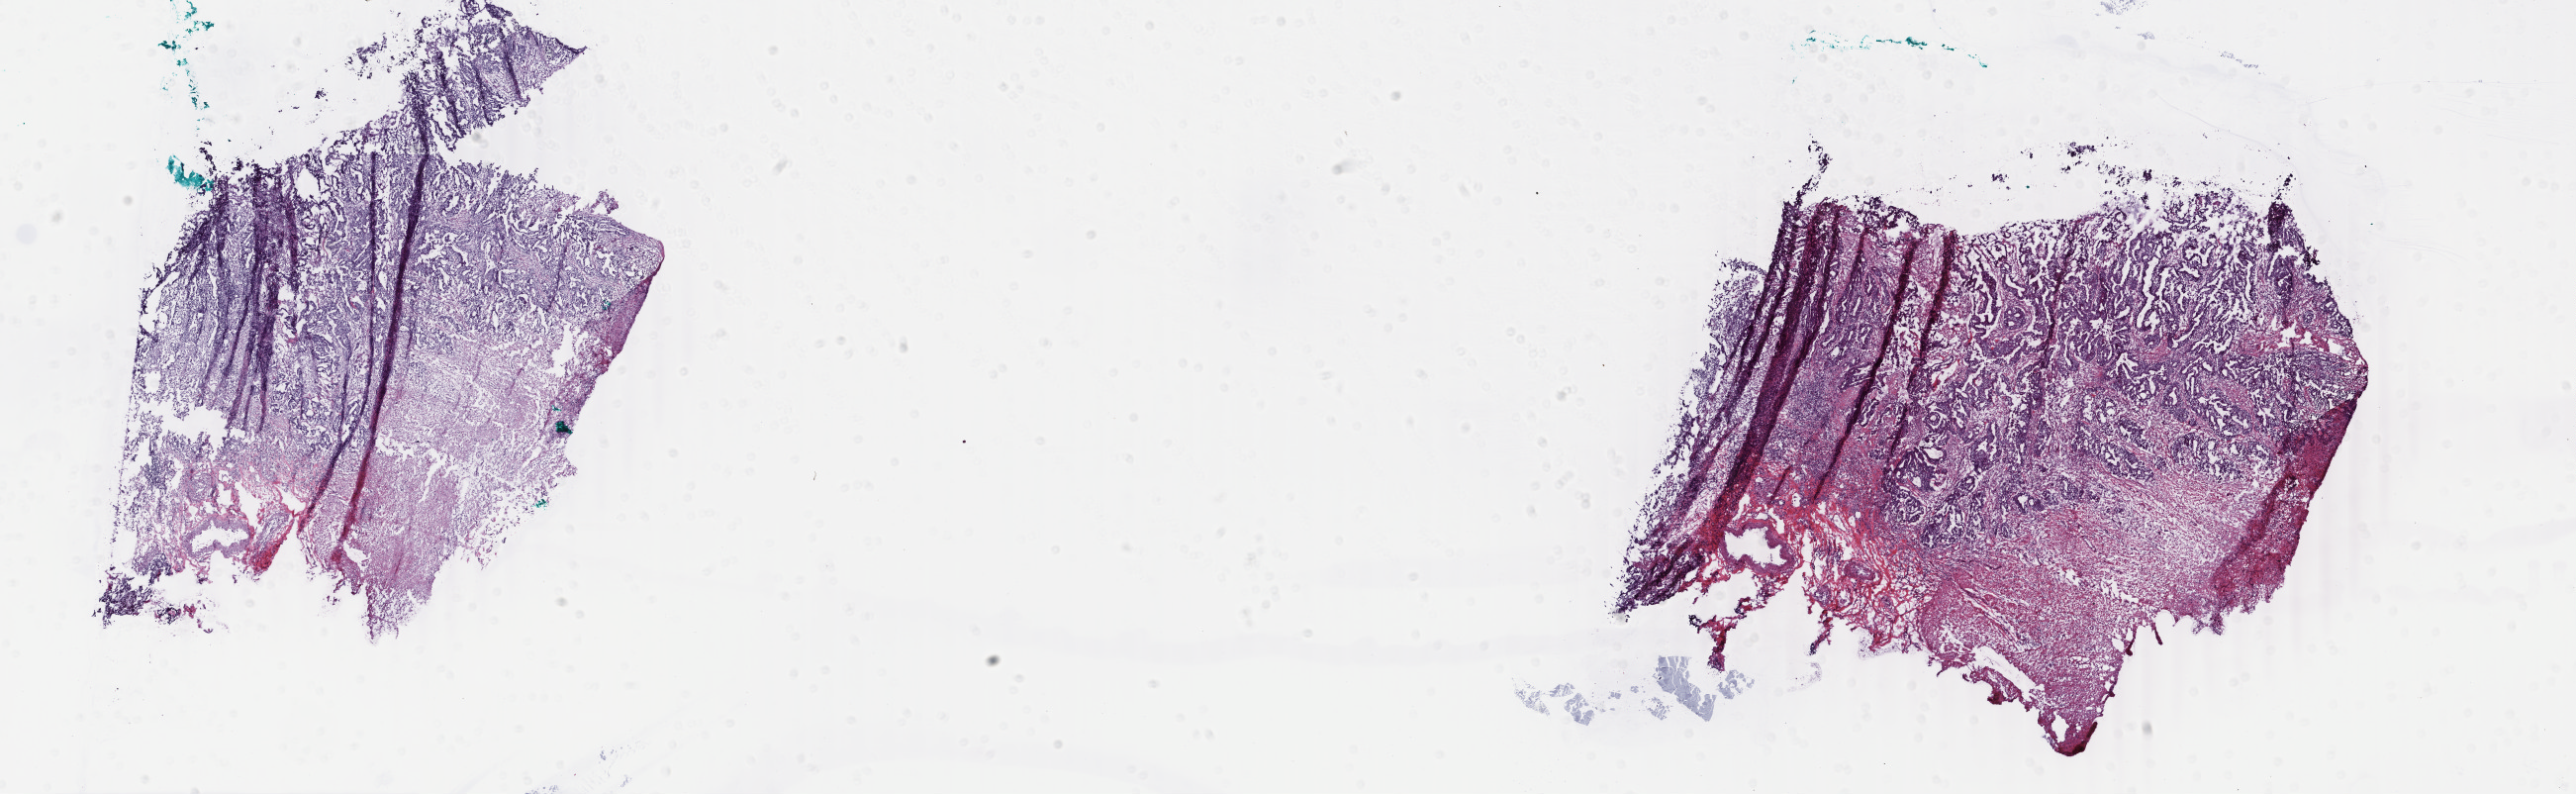
Digitized H&E-stained tissue section (whole slide), shown as a low-resolution overview of the whole scanned area (about 20.7 x 6.4 mm, from a 40x scan); frozen section; primary tumour sample from the colon. Male, age 75 years at initial diagnosis. Composition of this section per pathologist review: tumour cells 70%, tumour nuclei 80%, normal cells 0%, stromal cells 25%, necrosis 5%. Infiltration values recorded for this section: lymphocyte infiltration 8%, monocyte infiltration 2%, neutrophil infiltration 4%.
* pathologic diagnosis: Adenocarcinoma, NOS (ascending colon)
* AJCC pathologic stage: IIIA (6th edition)
* lymph nodes positive (case pathology): 3 of 31 examined